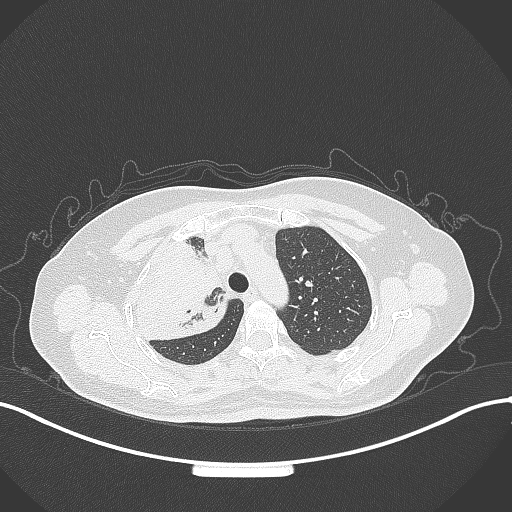
Chest CT, one axial slice; position 243 of 309 along the scan axis; reconstruction kernel B70f; 120 kVp; lung window (W 1500 / L -600 HU); 1 mm slice thickness; 512 × 512 image matrix, field of view 400 × 400 mm. Female patient, age 60 years. From the clinical record (not read from this slice): clinical TNM (as recorded): T3 N1 M1.
Annotated regions visible in this slice (rectangle marked by the reading radiologist):
- lung tumour (recorded histology: adenocarcinoma): bounding box [x1, y1, x2, y2] px = [125, 235, 233, 343]